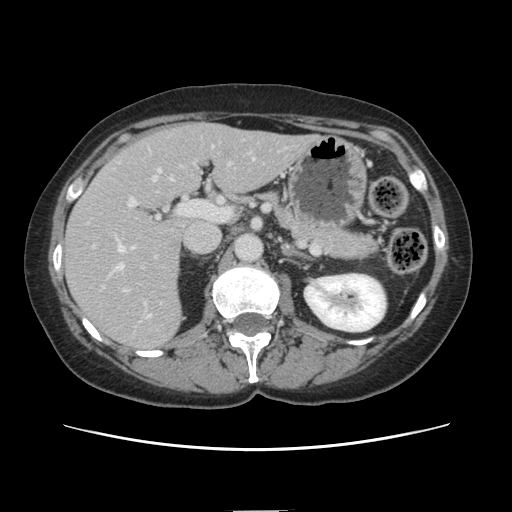
Contrast-enhanced abdominal CT, one axial slice; soft-tissue window (W 400 / L 40 HU); 512 × 512 image matrix. Female patient, age 63 years. Case-level facts recorded for this patient, not image findings: diagnosis: colorectal cancer liver metastases, imaged before liver resection; multiple liver metastases: yes; largest metastasis: 3.2 cm; chemotherapy before resection: yes.
Annotated regions visible in this slice (manually delineated by an expert):
- hepatic veins: box from (x=114, y=170) to (x=160, y=271) px
- liver: (x=67, y=124)–(x=311, y=351)
- planned liver remnant (the part of the liver to remain after resection): (x=175, y=124)–(x=312, y=194)
- portal vein (with intrahepatic branches): (x=123, y=174)–(x=210, y=318)